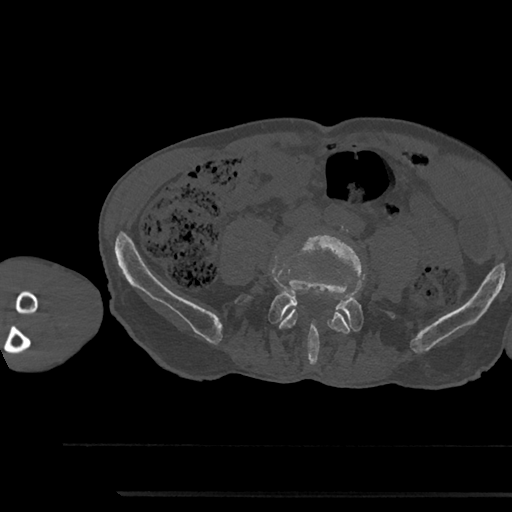
CT including the spine, one axial slice. Bone window (W 1800 / L 400 HU). 512 × 512 image matrix, field of view 367 × 367 mm. Male patient, age 79 years. Case-level facts recorded for this patient, not image findings: primary cancer: prostate.
Outlined on this slice (semi-automatic segmentation, software-assisted and operator-edited):
- L4 vertebra: bounding box [x1, y1, x2, y2] px = [279, 234, 364, 334]
- L5 vertebra: [236, 278, 395, 363]